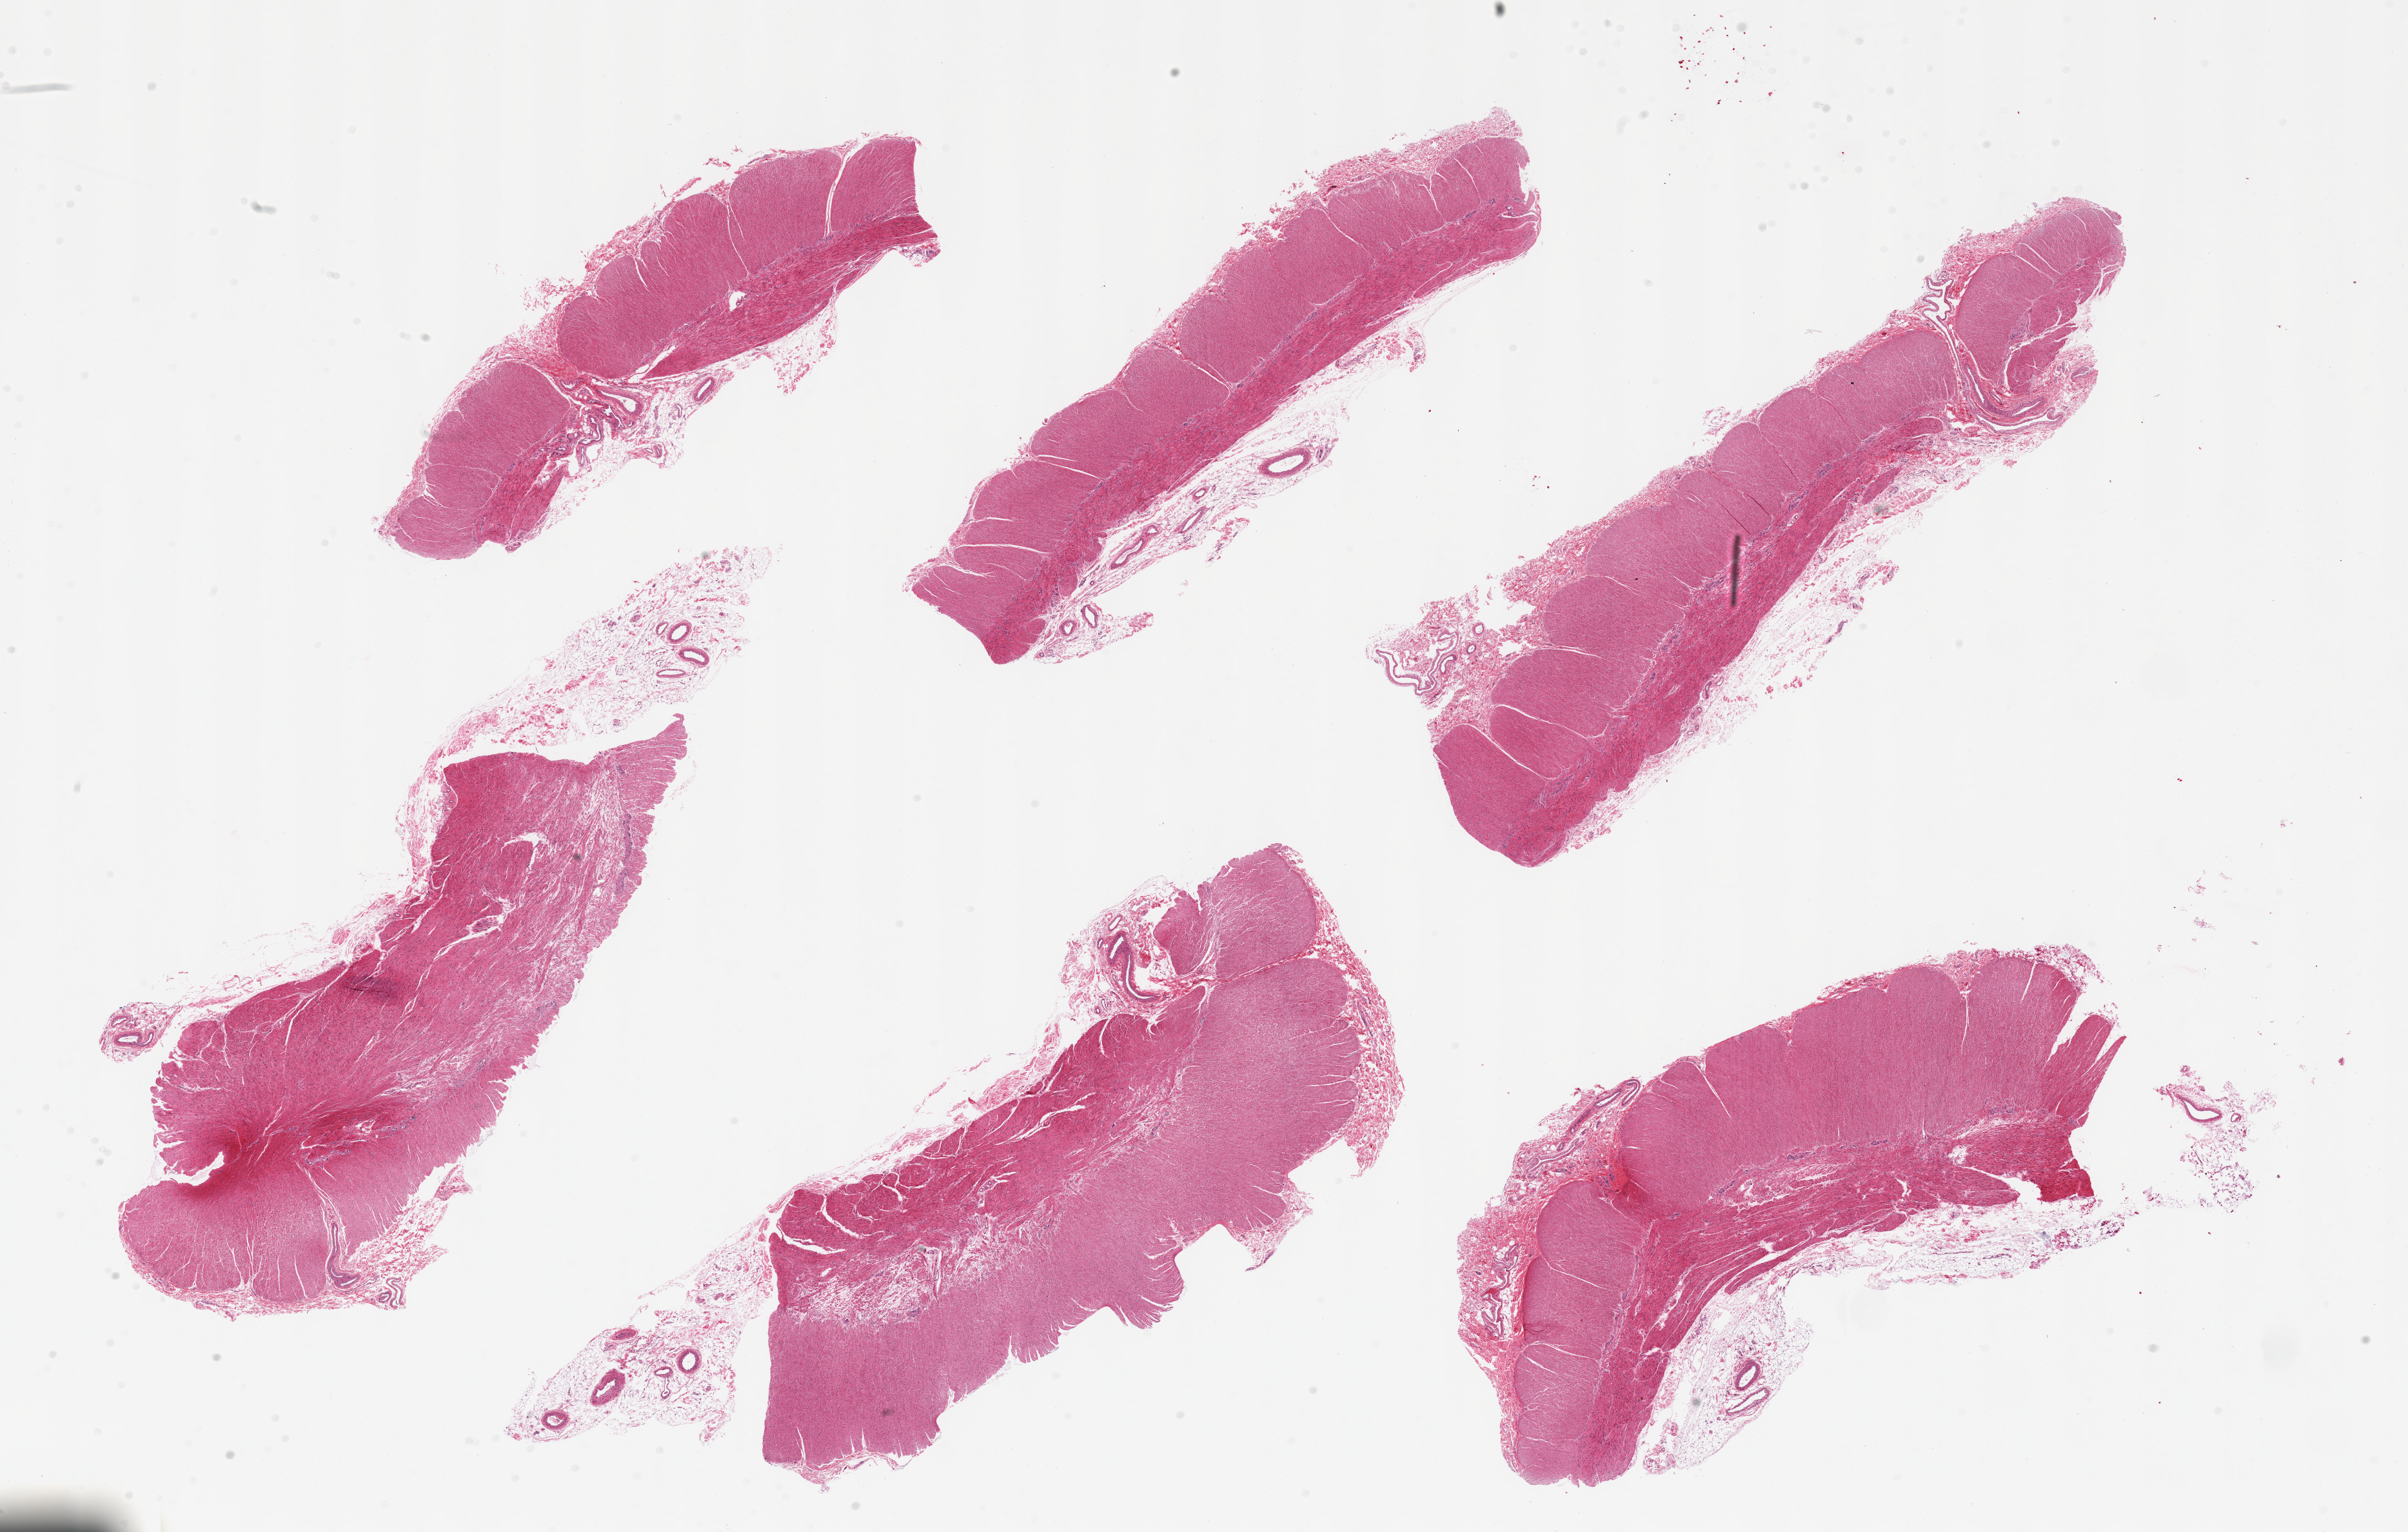
Digitized H&E-stained section, brightfield, whole scanned area (about 29.5 x 18.8 mm, acquisition: 20x scan) shown as a low-resolution overview, PAXgene-fixed, paraffin-embedded tissue, section of sigmoid colon (target tissue), tissue donor sample. Female donor.
Review note (as recorded): 6 pieces, confirmed target muscularis, adherent fatty nubbins up to ~3mm.